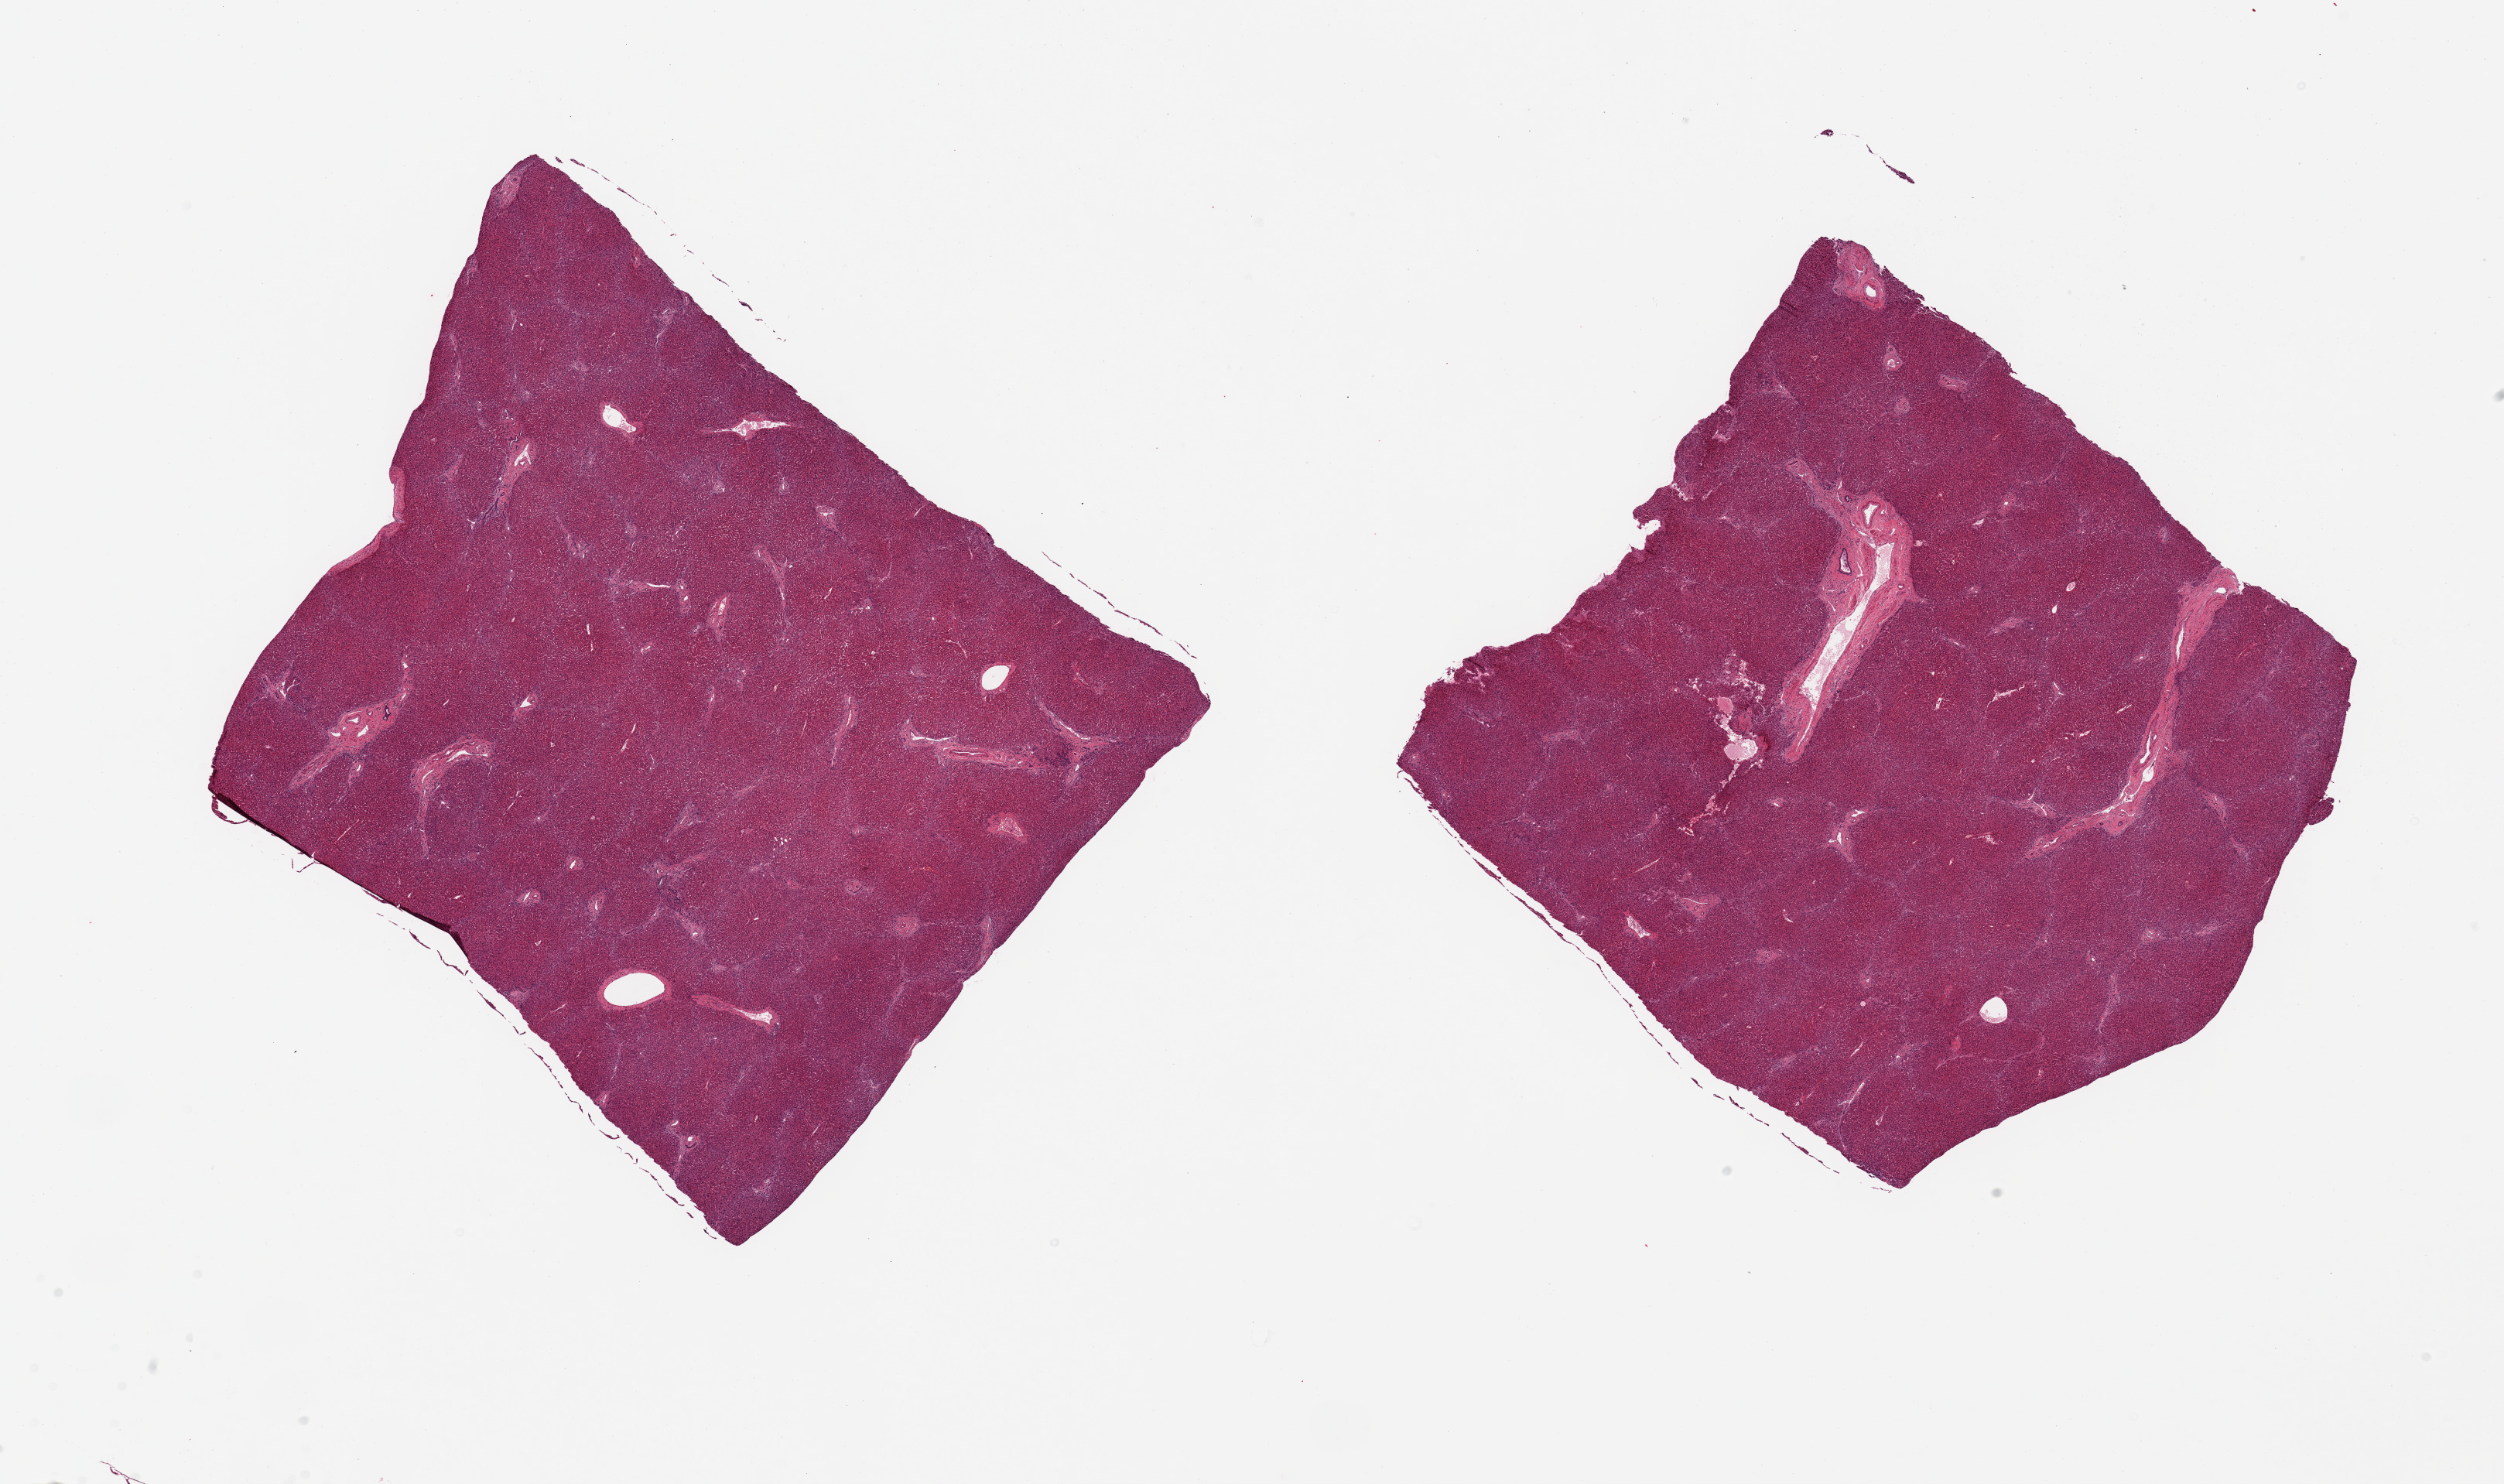
H&E whole-slide image — a low-resolution overview of the entire scanned area, about 25.6 x 15.2 mm (slide scanned at 20x), PAXgene-fixed paraffin-embedded (PFPE) section, target tissue: liver, tissue donor sample. Donor sex: male.
- reviewer comment on this tissue sample: 2 pieces